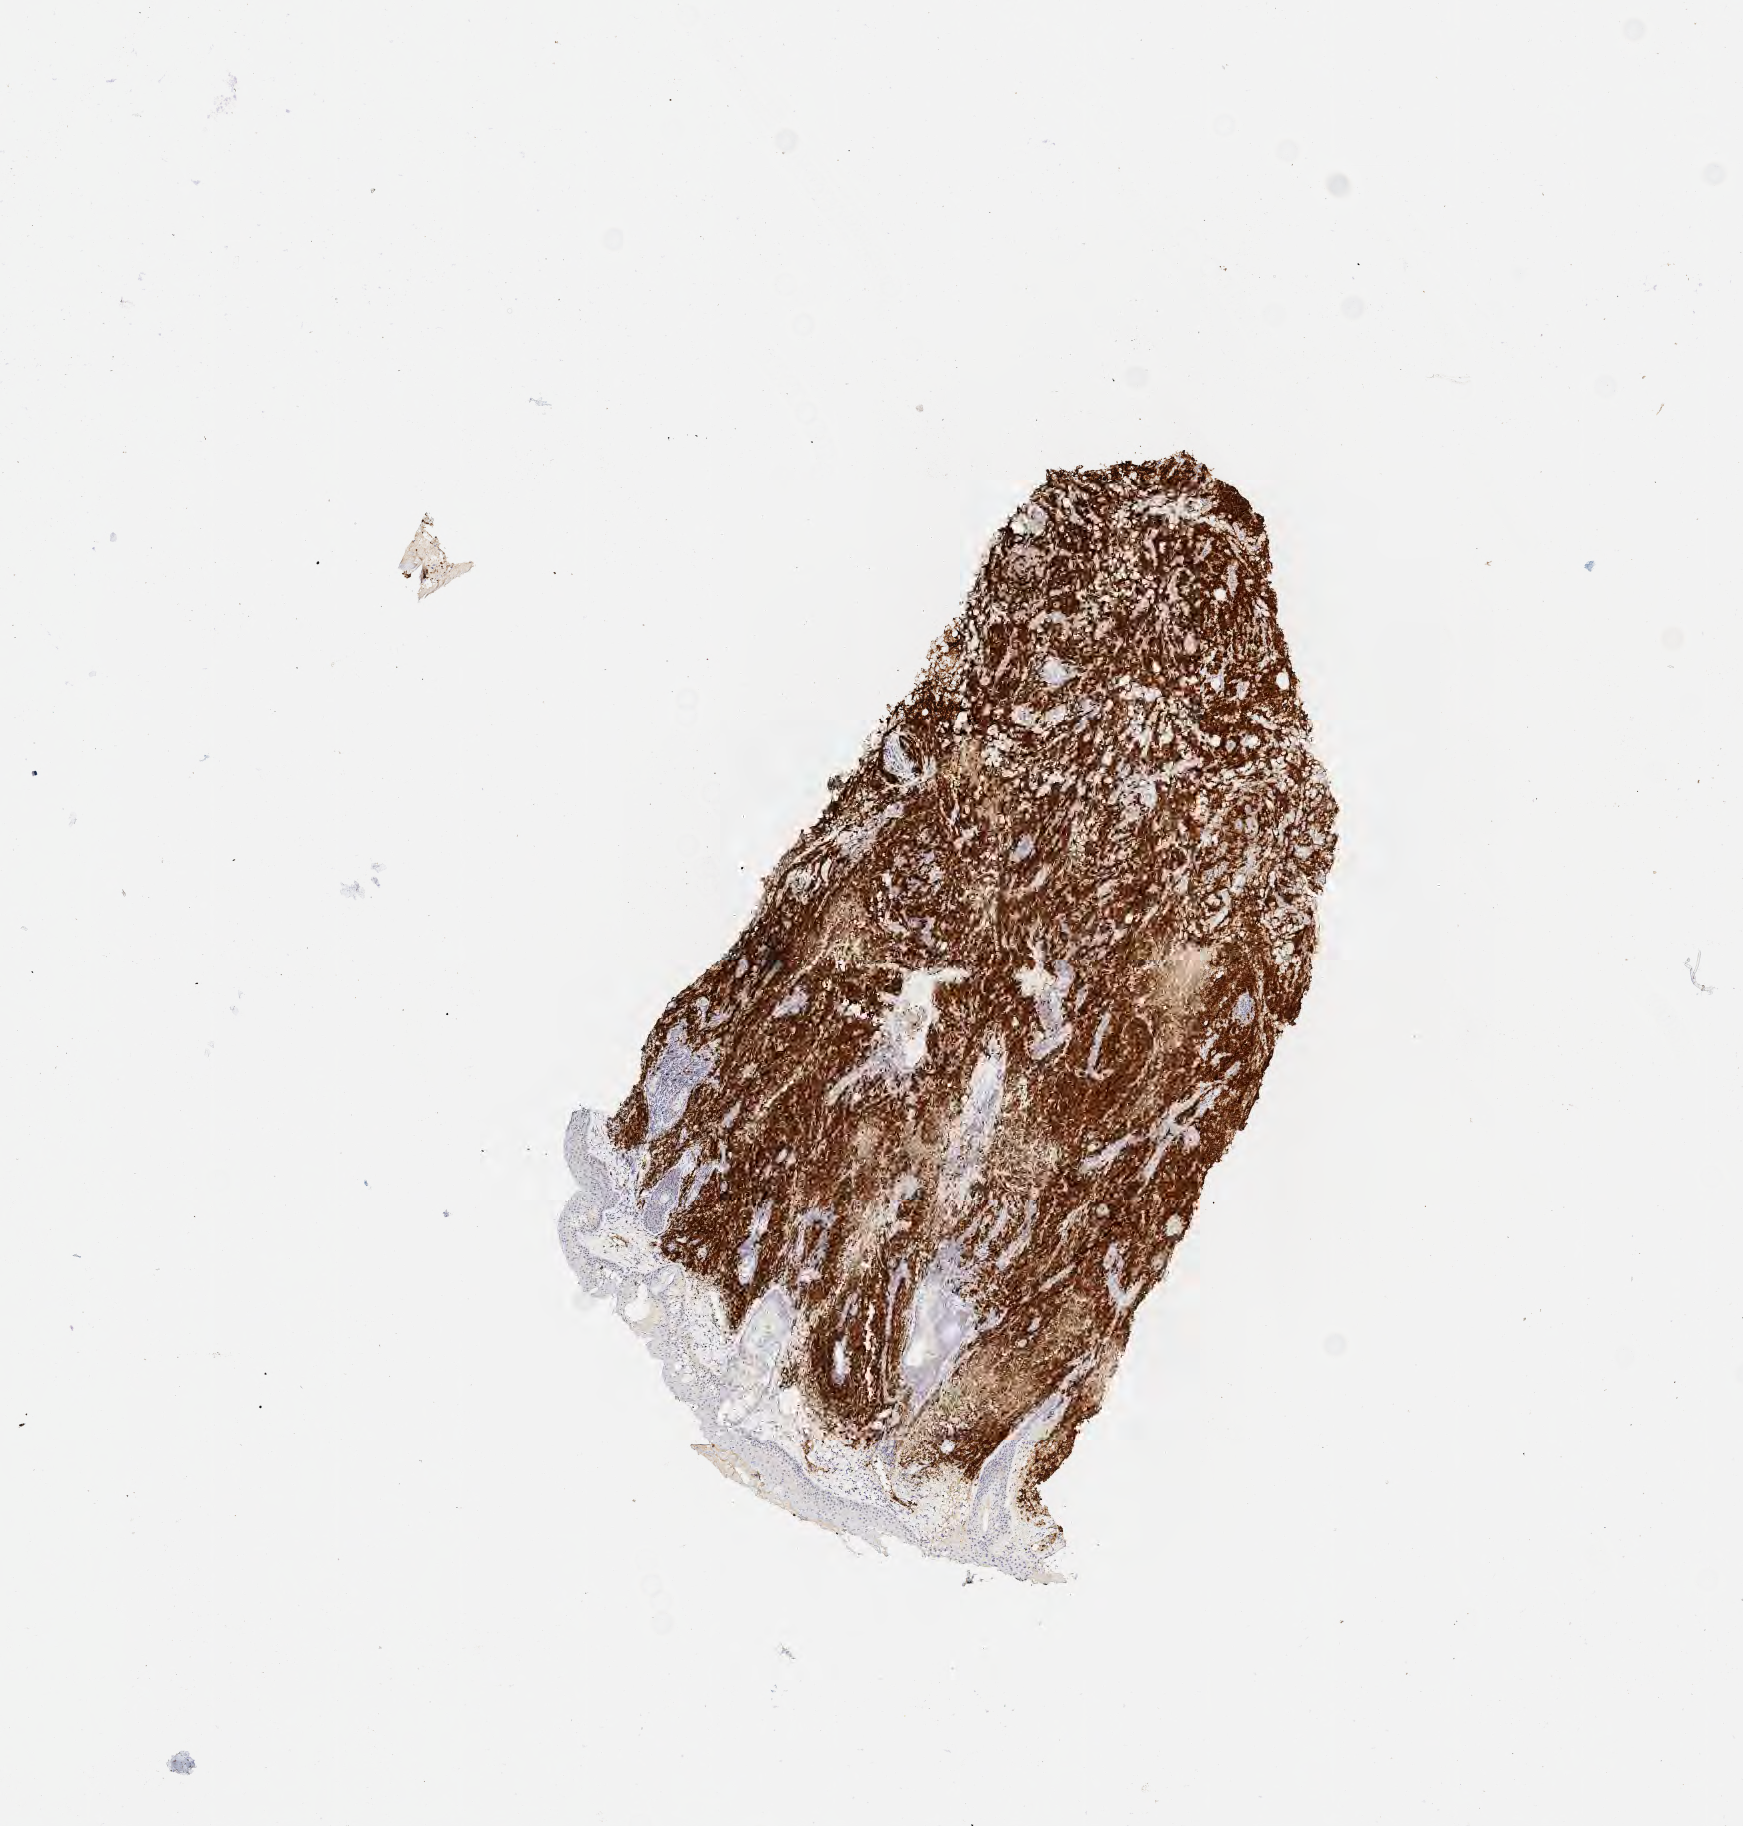
Whole-slide image, immunohistochemical stain for CD79a — low-resolution overview of the scanned area, about 7.0 x 7.4 mm; tumor tissue. Male patient, aged 41.
* diagnosis: Diffuse large B-cell lymphoma, NOS